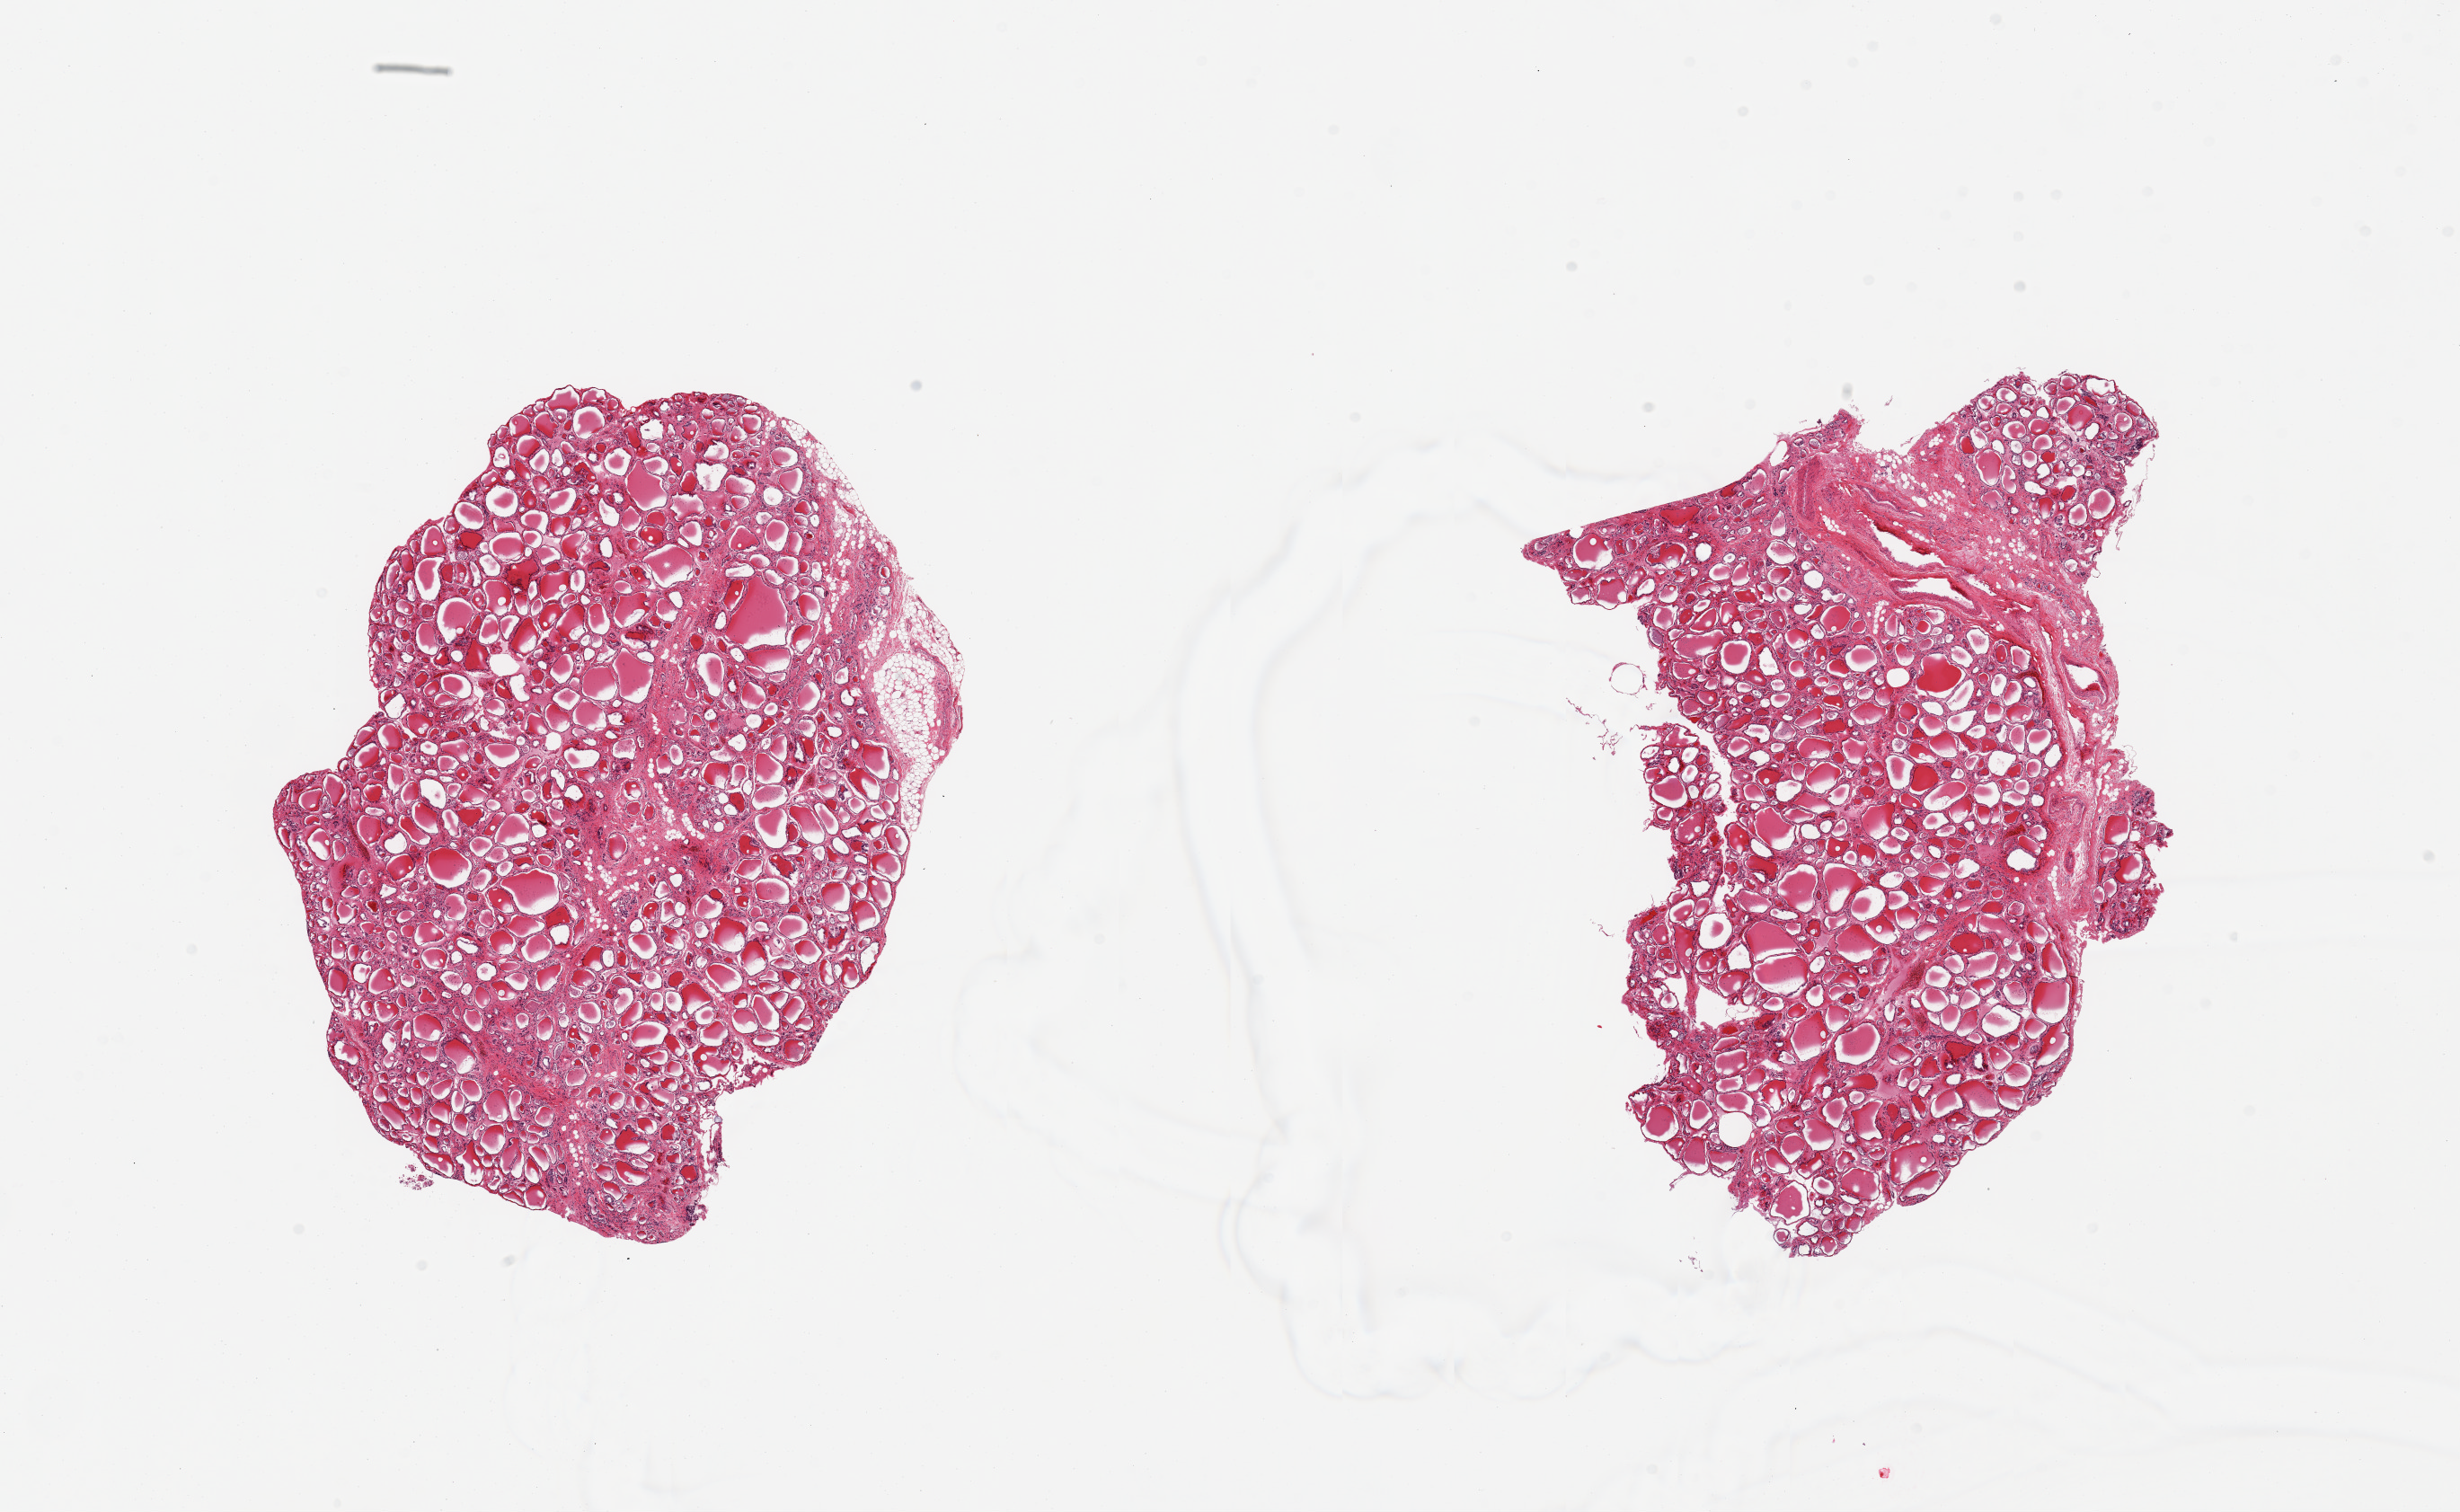
Whole-slide image, haematoxylin and eosin stain, low-resolution overview of the scanned area, about 21.7 x 13.3 mm, PAXgene-fixed paraffin-embedded (PFPE) section, sampled site (target tissue): thyroid, tissue donor sample. Donor: male.
Review note (as recorded): 2 pieces, mild goitre, regressive changes.